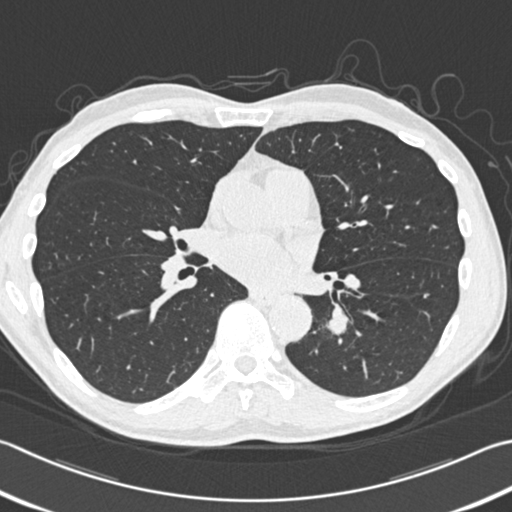
Low-dose screening chest CT, one axial slice; slice 173 of 354 in the series (ordered by position); reconstruction kernel B30f; 120 kVp; lung window (W 1500 / L -600 HU); 512 × 512 image matrix, field of view 346 × 346 mm.
Annotated regions visible in this slice (outlined manually by an expert reader):
- lesion 1 (tumor, lower lobe of left lung): bounding box <328,316,347,335> (left, top, right, bottom; pixels)